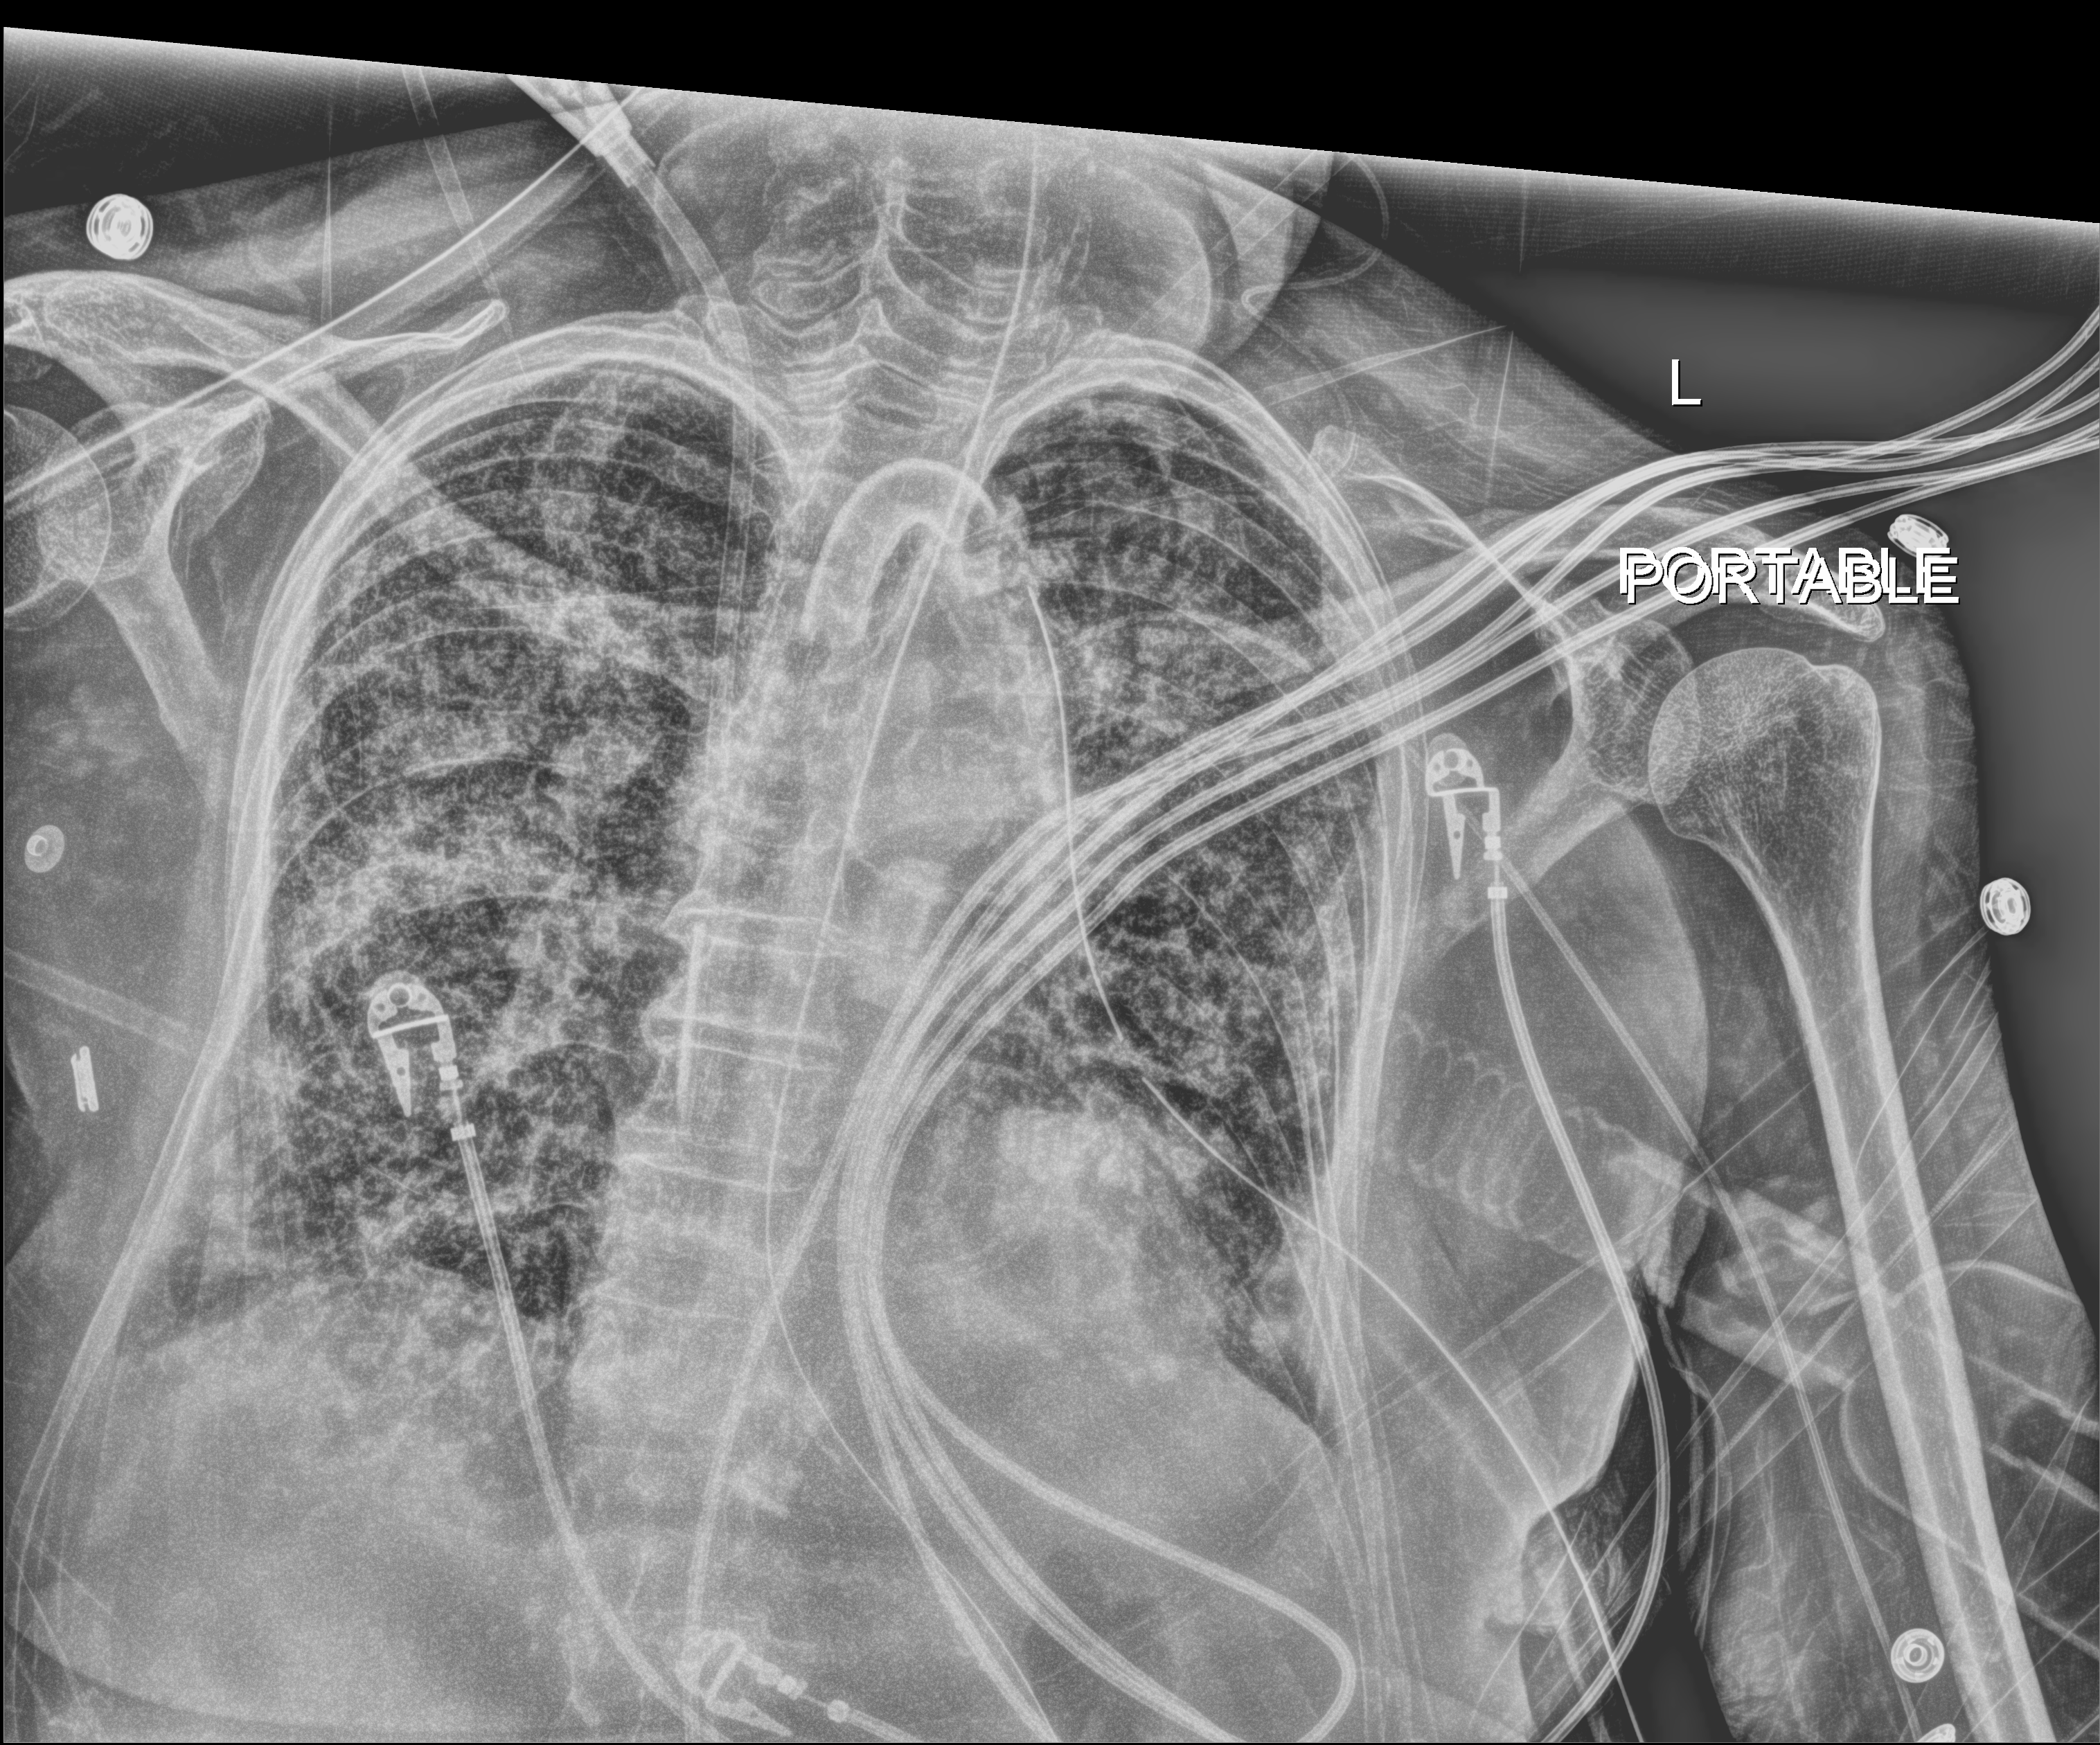
Portable chest radiograph; anteroposterior (AP) projection. Patient hospitalised with COVID-19; female, aged 75–90 years.
From the hospital-stay record, not from the radiograph (when in the stay this image was taken is not recorded):
- length of hospital stay: 70 days